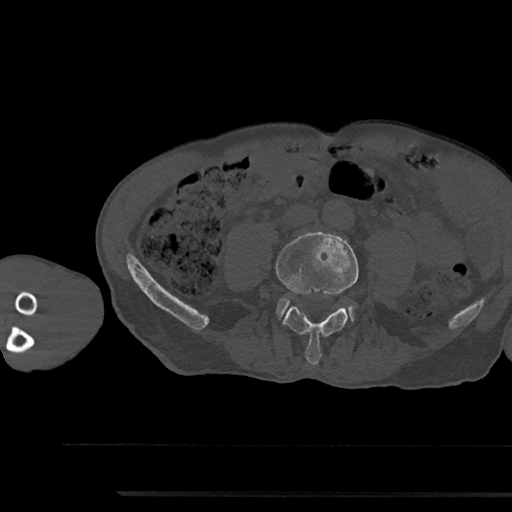
CT including the spine, one axial slice; position 395 of 797 along the scan axis; reconstruction kernel Br40s/3; bone window (W 1800 / L 400 HU); 0.5 mm slice thickness; 512 × 512 image matrix, field of view 367 × 367 mm. Male patient, age 79 years. From the clinical record (not read from this slice): primary cancer: prostate.
Structures marked on this image (semi-automatically segmented with operator editing):
- L4 vertebra: bounding box (x1, y1, x2, y2) in pixels: (276, 232, 359, 365)
- L5 vertebra: (278, 298, 354, 319)